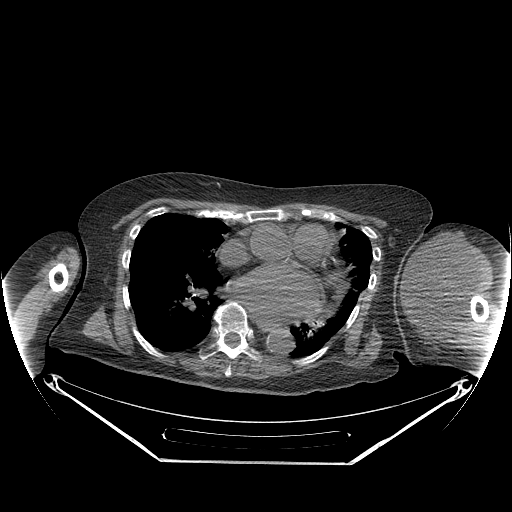
CT of an extremity soft-tissue mass (from a PET/CT study), one axial slice; slice 168 of 267 in the series (ordered by position); soft-tissue window (W 400 / L 40 HU); 3.75 mm slice thickness; 512 × 512 image matrix, field of view 500 × 500 mm. Female patient. Case-level facts recorded for this patient, not image findings: histological type: pleiomorphic leiomyosarcoma; grade: high; site of the primary tumour: left biceps.
Annotated regions visible in this slice (expert contour drawn on MRI and transferred to this co-registered scan by the dataset authors):
- gross tumour volume including surrounding oedema: bounding box [x1, y1, x2, y2] px = [402, 233, 487, 330]
- gross tumour volume (mass): [402, 233, 480, 325]